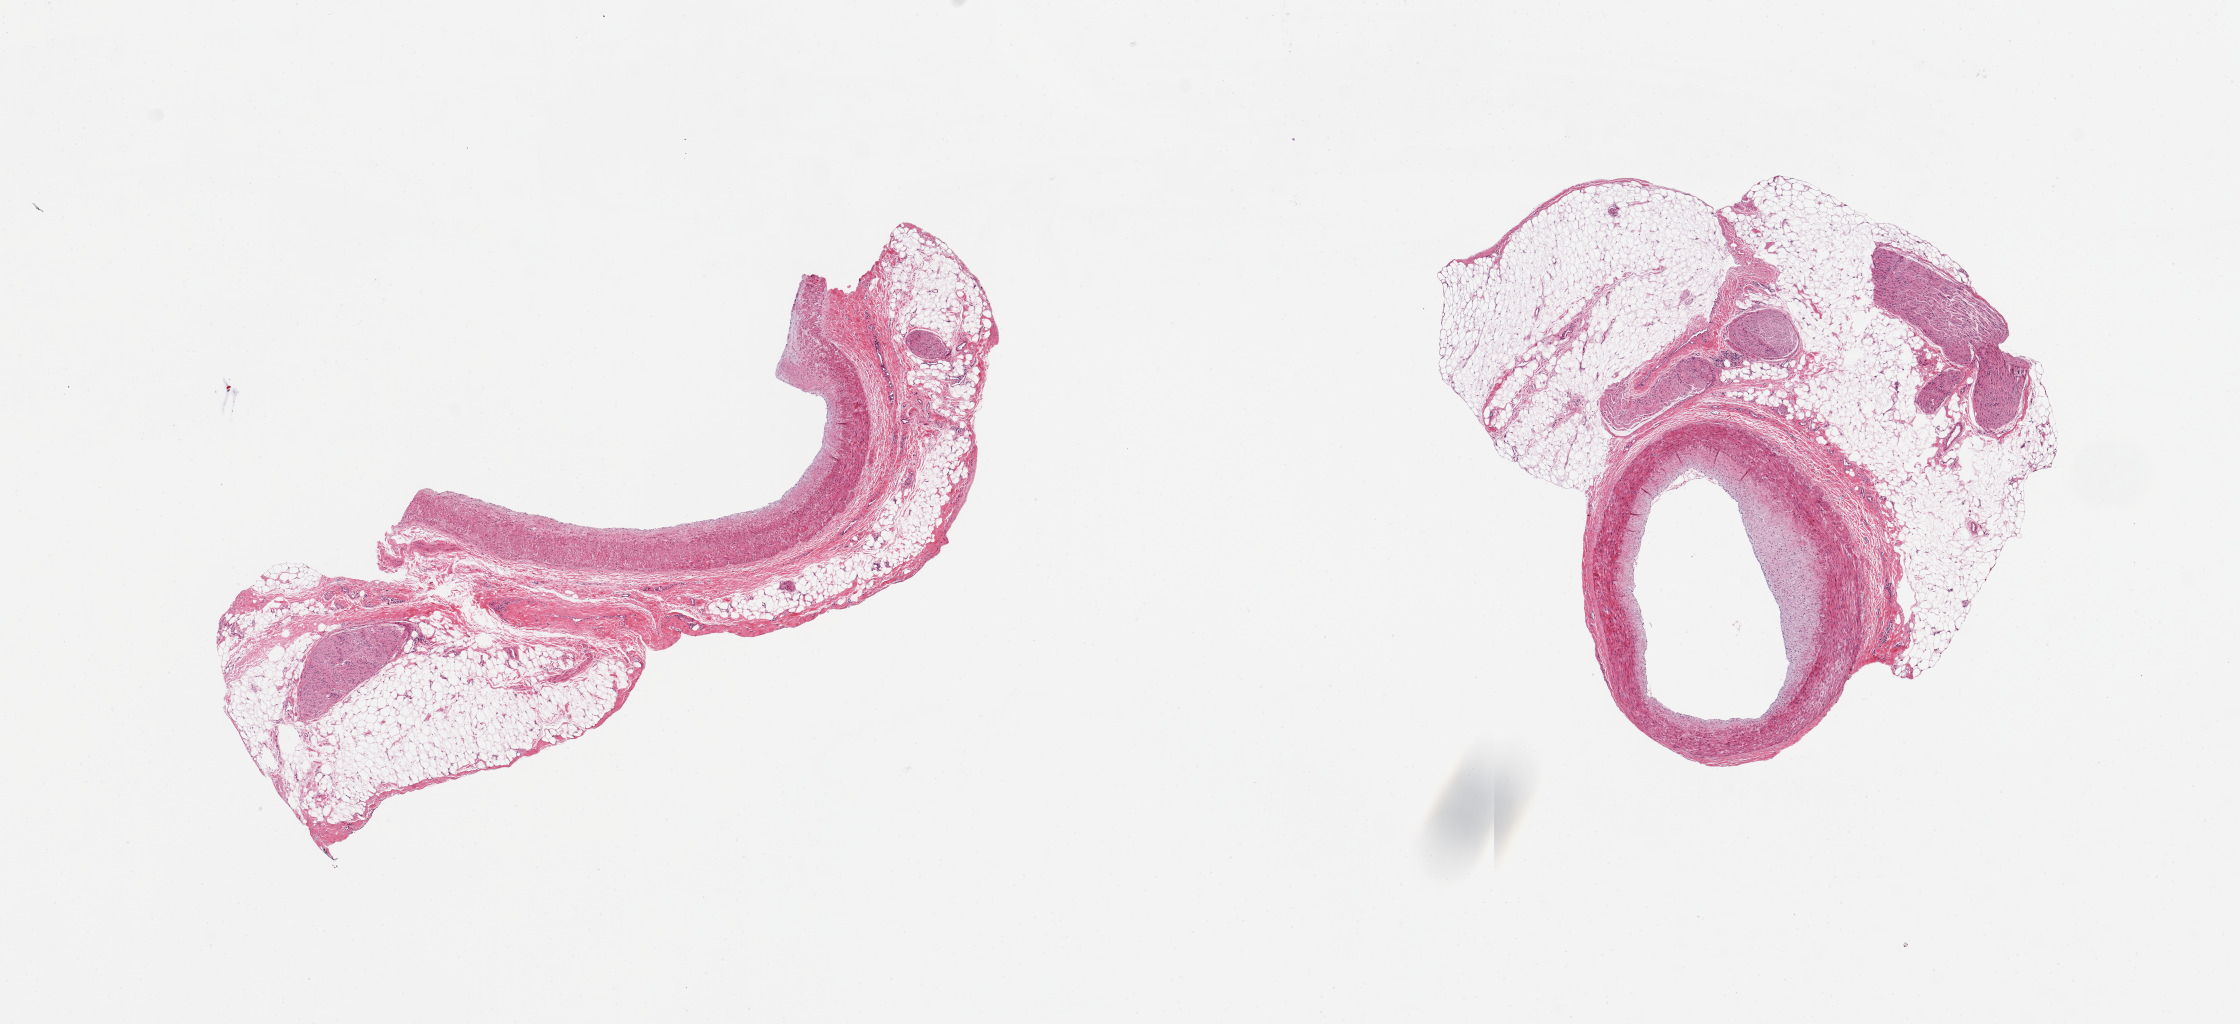
Digitized hematoxylin and eosin (H&E)-stained section, shown as a low-resolution overview of the whole scanned area (about 17.7 x 8.1 mm). PAXgene-fixed, paraffin-embedded tissue. Section of coronary artery (target tissue). Donor tissue sample. Male donor.
- reviewer comment on this tissue sample: 2 pieces, one distorted ~3mm d with adherent nubbins fat/fibrous tissue up to 2x5mm